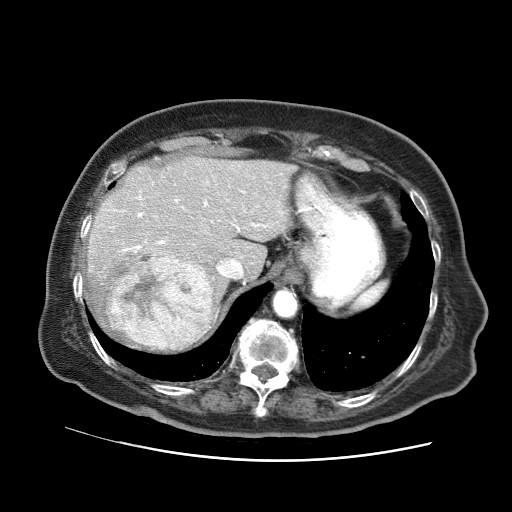
Contrast-enhanced abdominal CT (liver protocol), one axial slice. Position 51 of 73 along the scan axis. Reconstruction kernel STANDARD. Soft-tissue window (W 400 / L 40 HU). 512 × 512 image matrix, field of view 380 × 380 mm. From the clinical record (not read from this slice): diagnosis: hepatocellular carcinoma (patient treated with transarterial chemoembolisation; whether this scan precedes or follows treatment is not stated here); TNM stage (as recorded): Stage-I; Child-Pugh class: A; tumour differentiation: well differentiated.
Structures marked on this image (semi-automatically segmented with operator editing):
- liver parenchyma outside the tumour (the mass and vessels are separate outlines, so this box may not span the whole liver): bounding box (x1, y1, x2, y2) in pixels: (82, 156, 296, 351)
- mass: (104, 252, 213, 349)
- liver vessels: (122, 191, 266, 252)